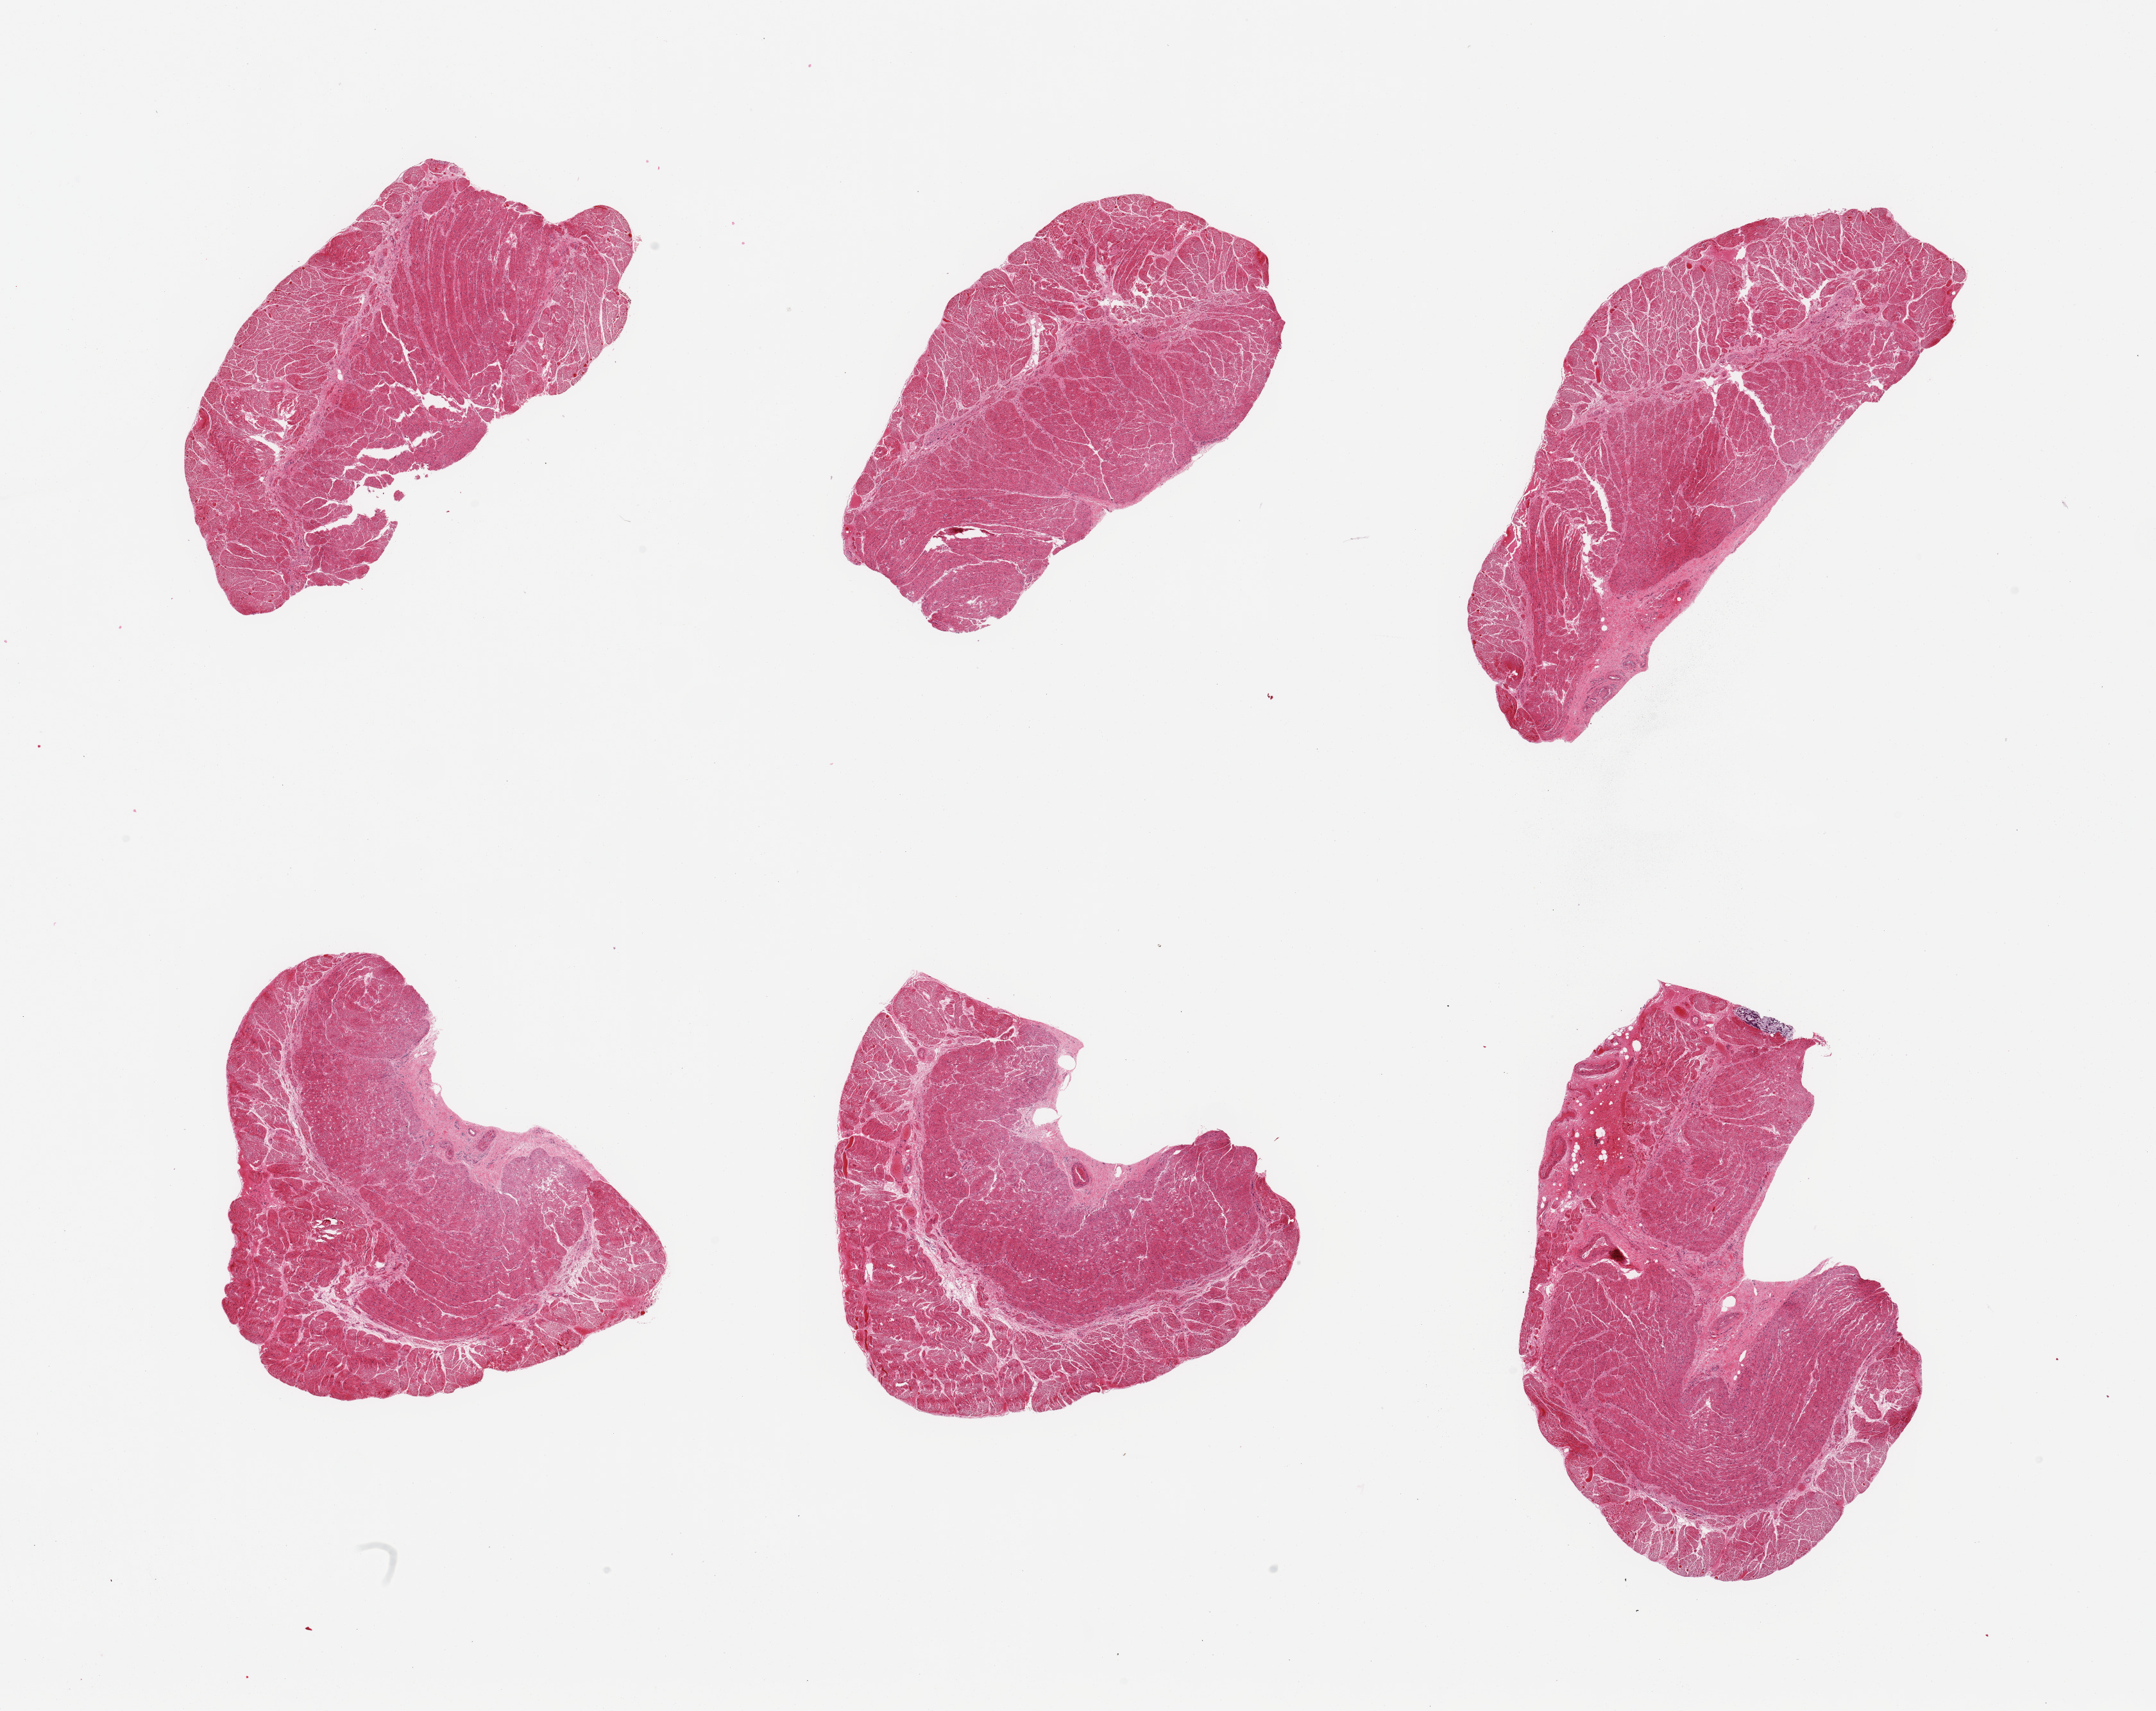
Digitized hematoxylin and eosin (H&E)-stained section — whole scanned area (about 26.6 x 21.1 mm, from a 20x scan) shown as a low-resolution overview; PAXgene-fixed, paraffin-embedded tissue; section of esophageal muscle (target tissue); donor tissue sample. Male donor.
Review note (as recorded): 6 pieces; well trimmed target muscularis.